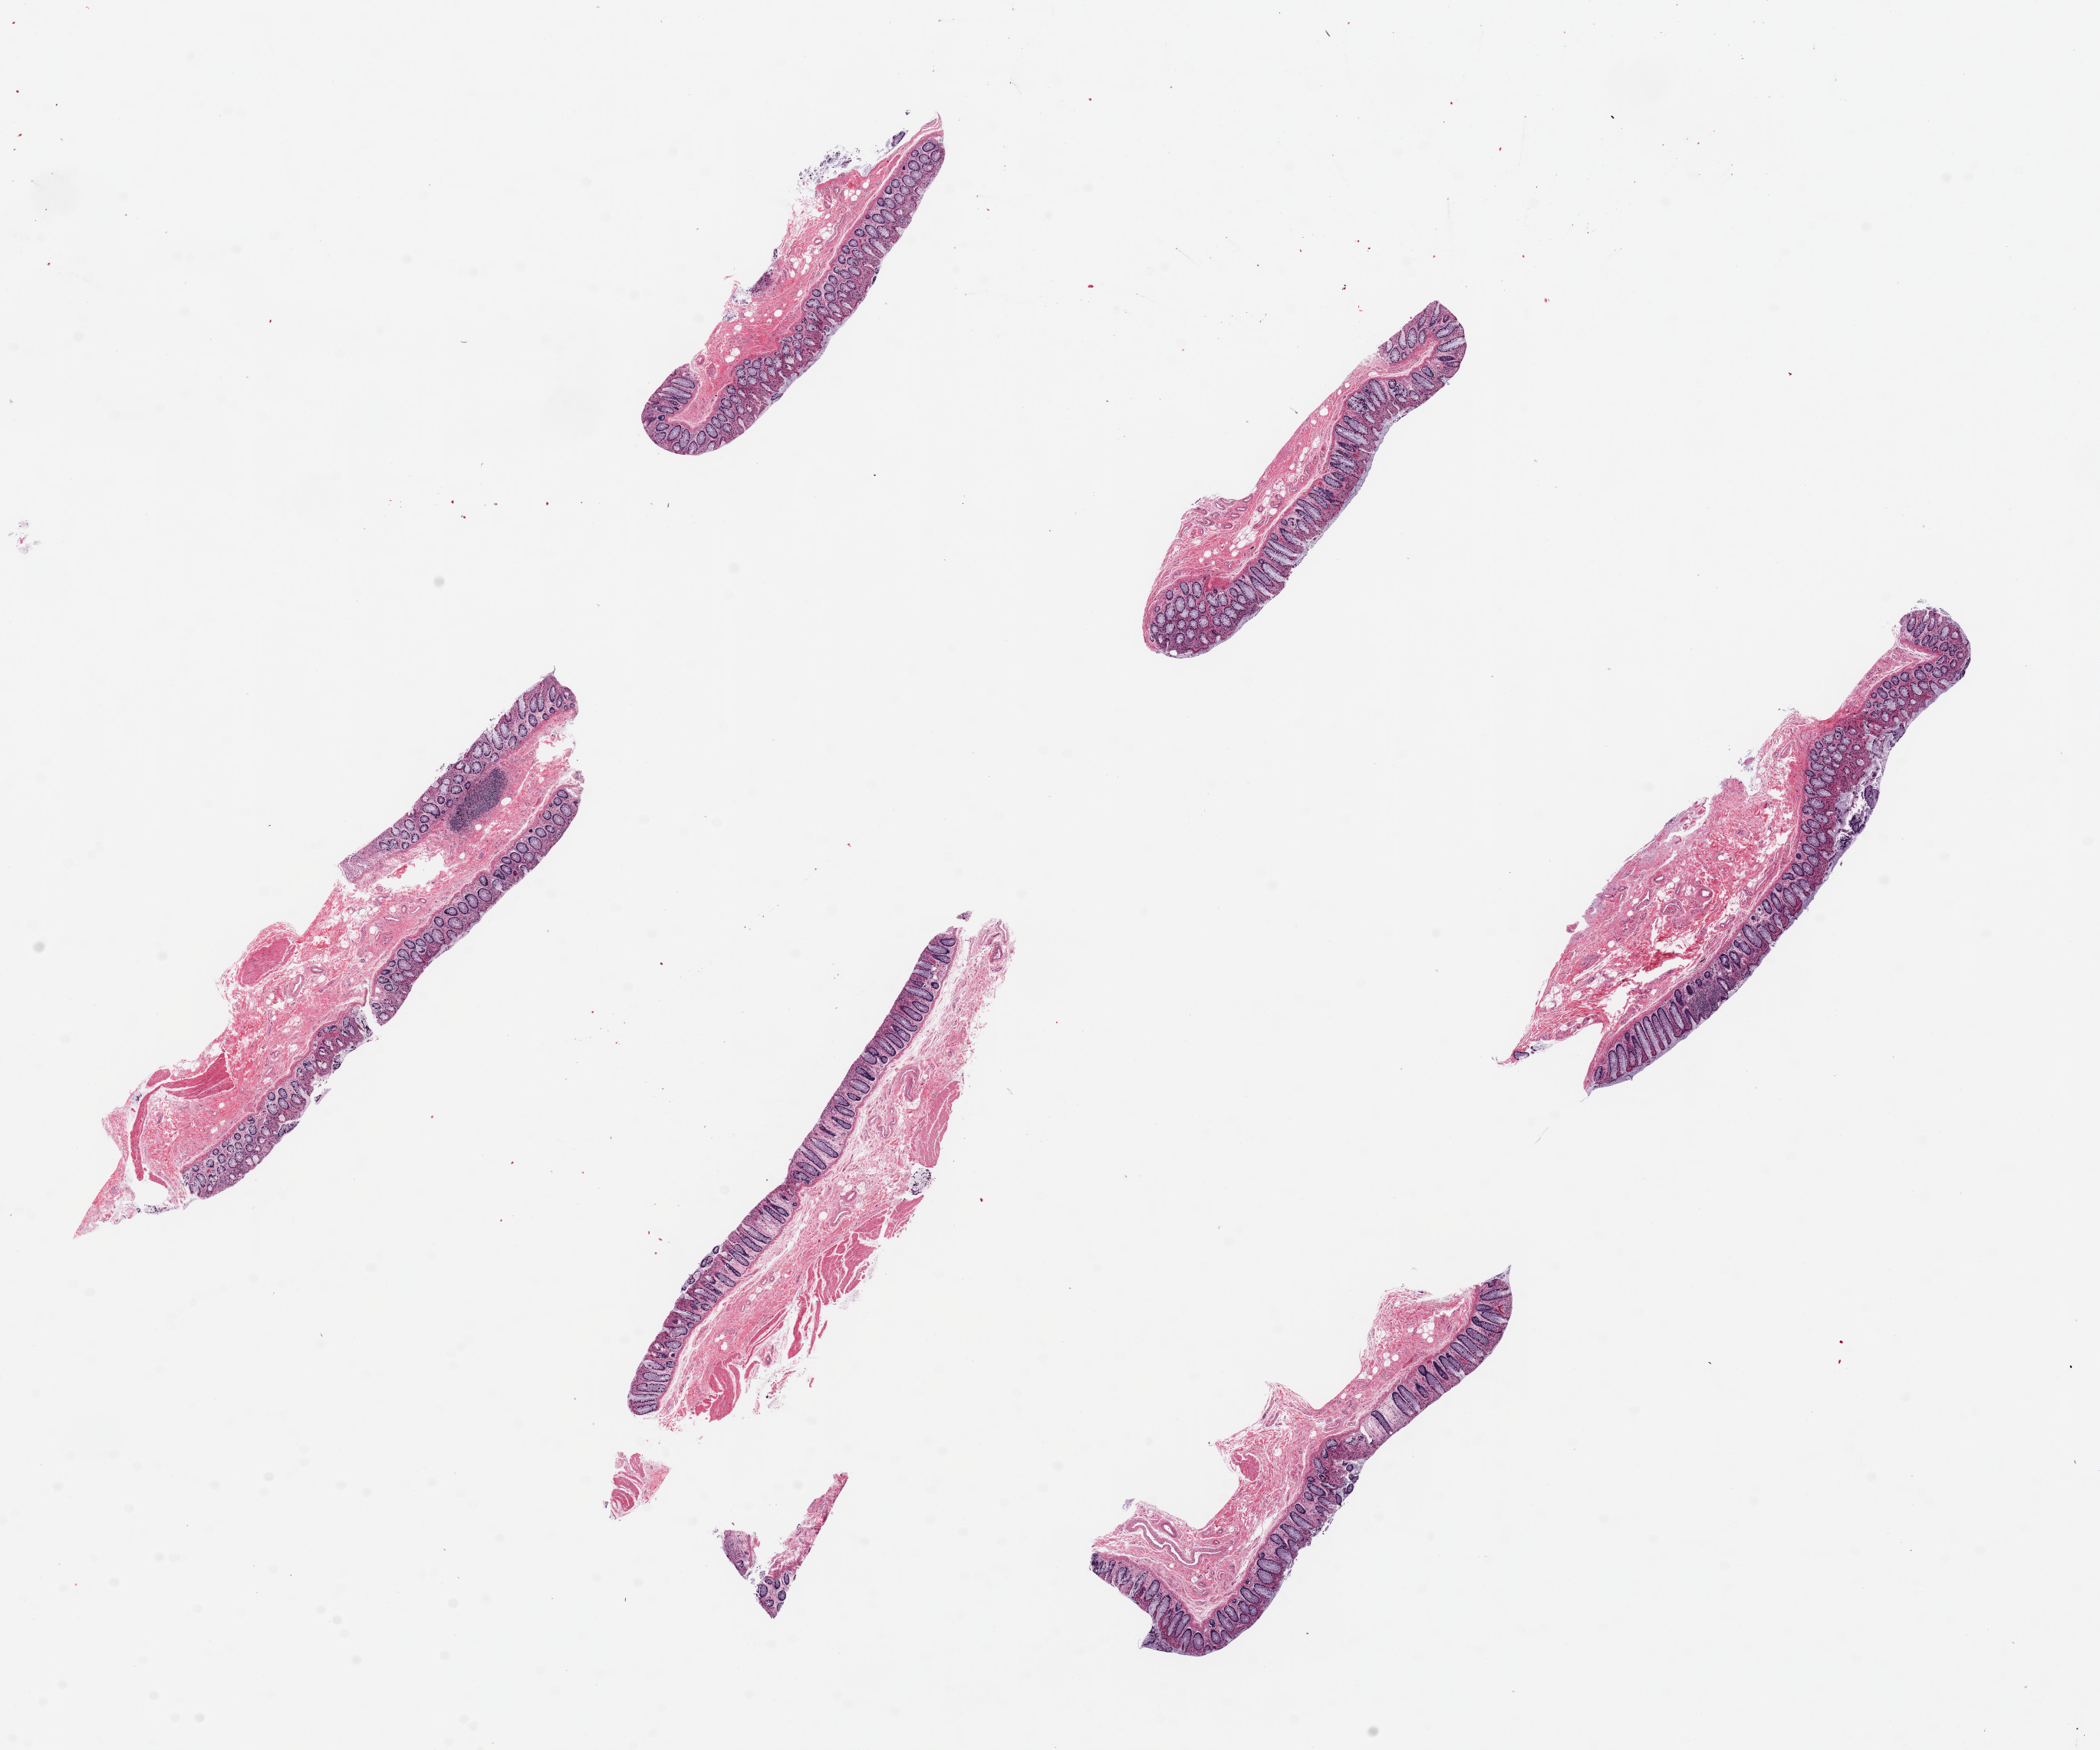
Digitized H&E-stained section, brightfield, whole scanned area (about 21.7 x 18.1 mm, slide scanned at 20x) shown as a low-resolution overview. PAXgene-fixed, paraffin-embedded tissue. Sampled site (target tissue): sigmoid colon. Tissue donor sample. Male donor.
Pathologist's review note for this sample: 6 pieces ~6x1mm mucosa is ~25% of thickness.